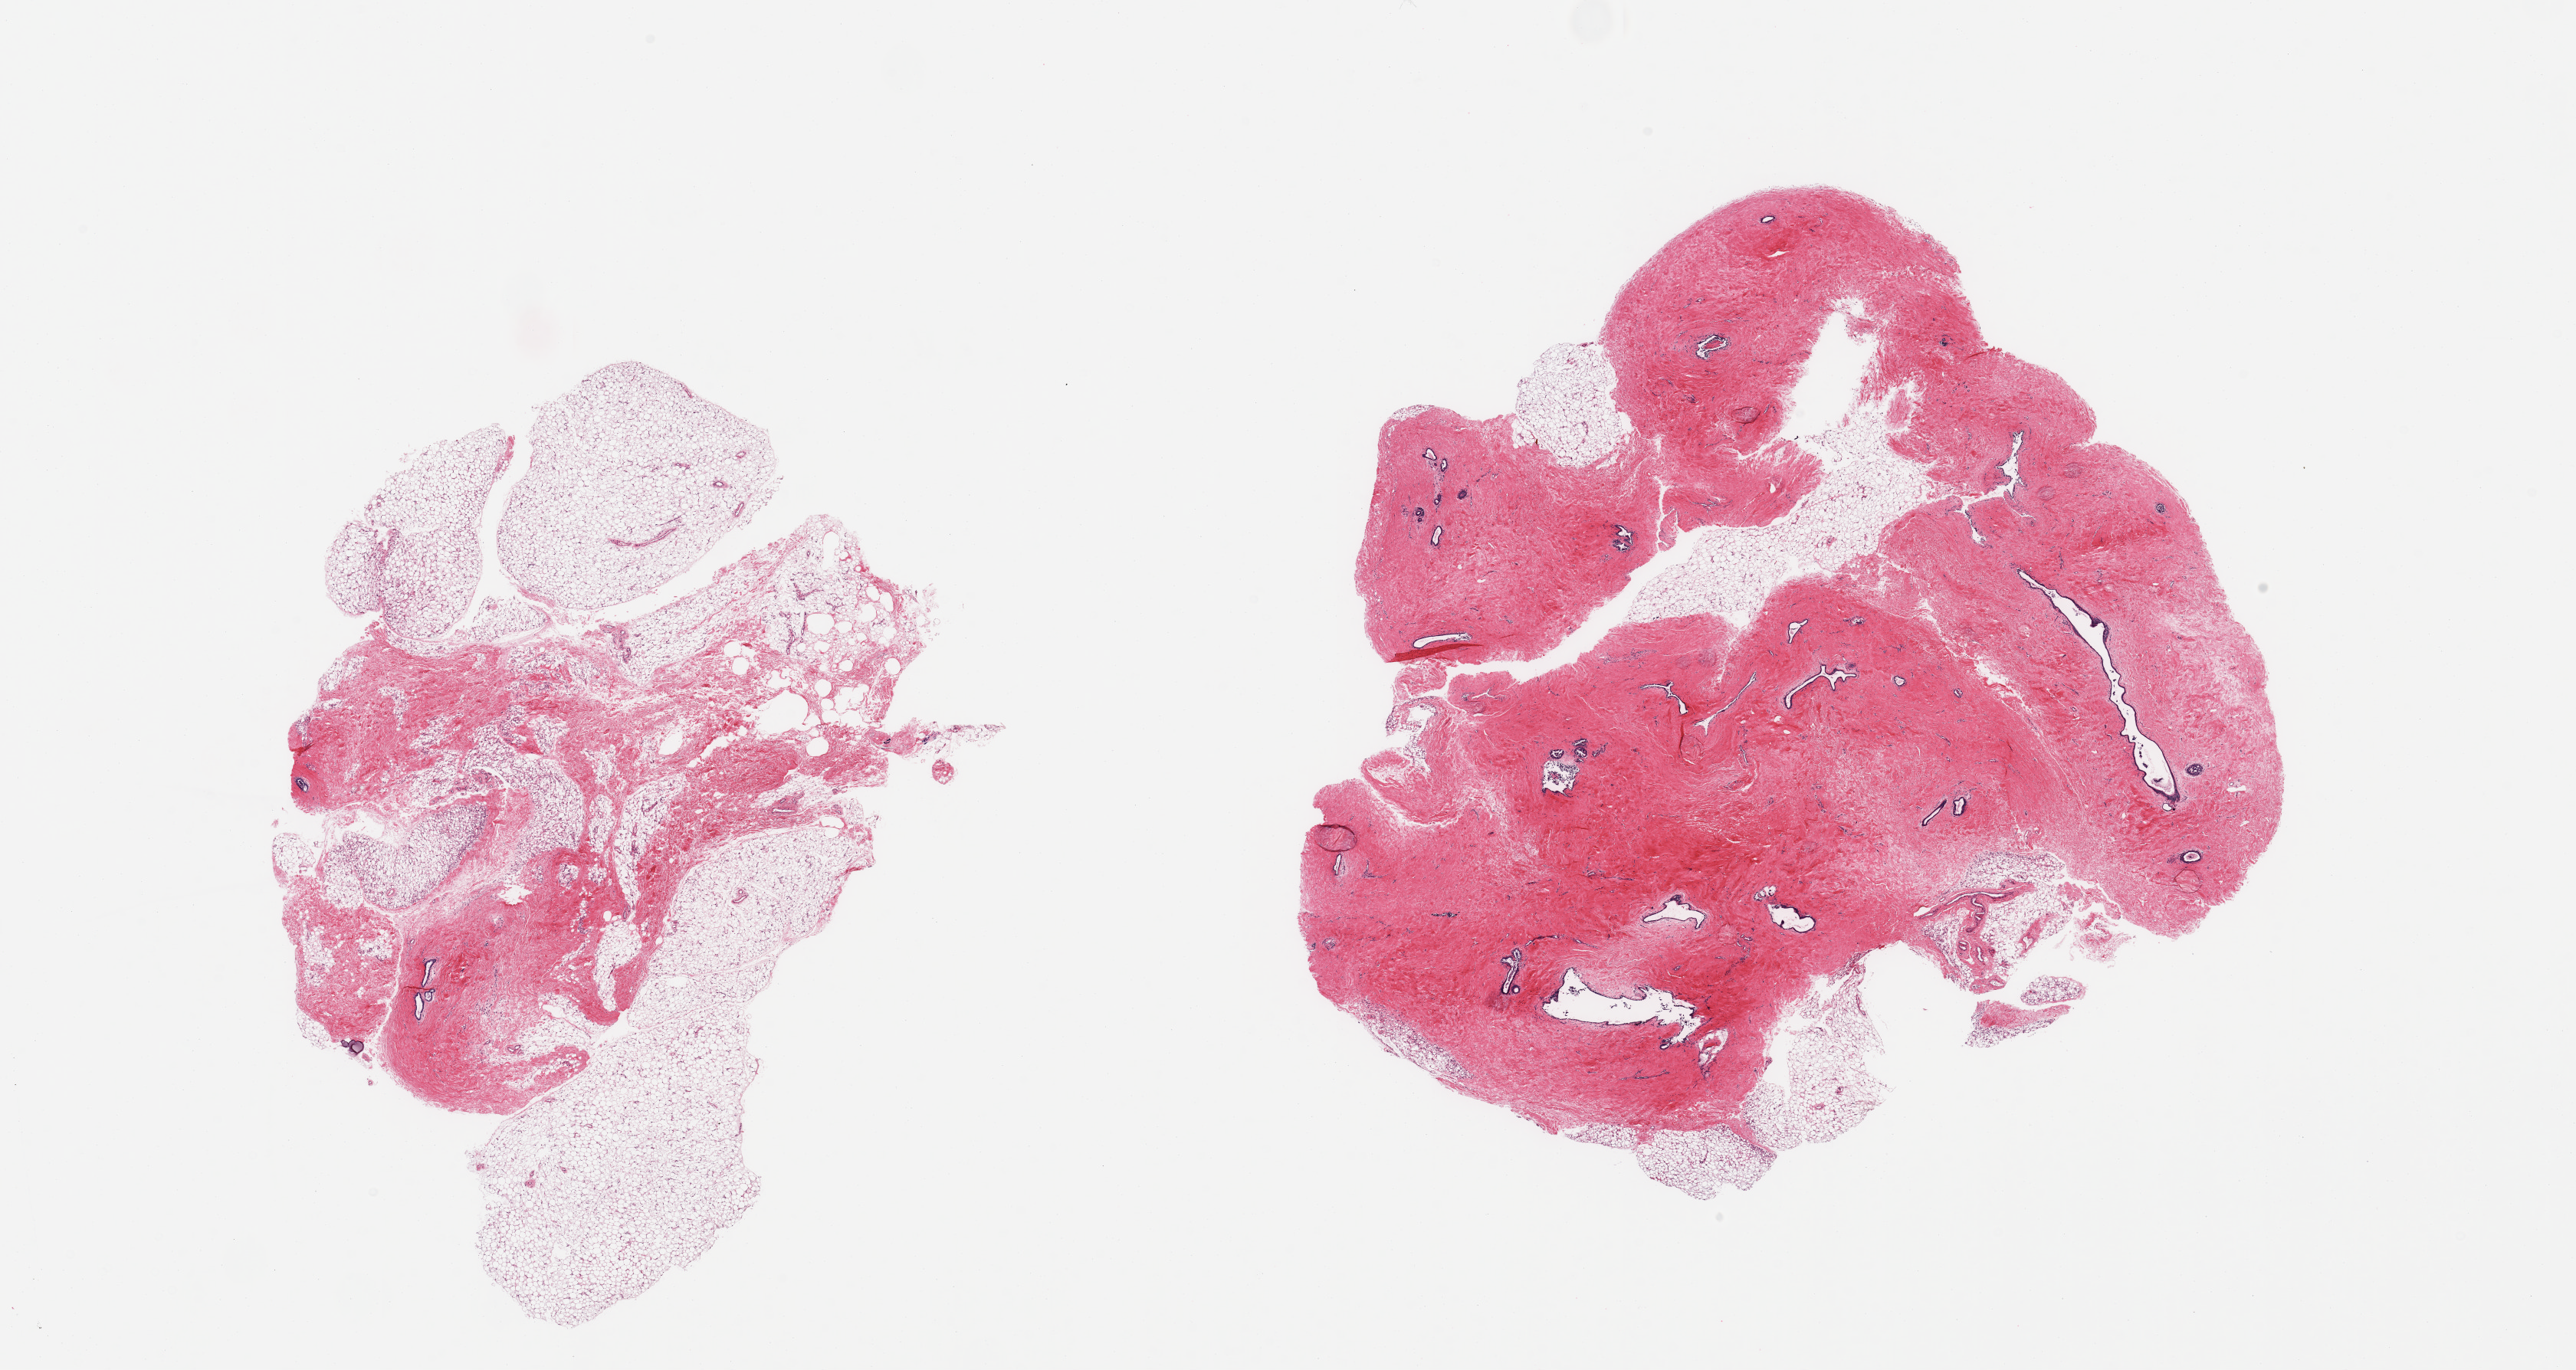
H&E whole-slide image — shown as a low-resolution overview of the whole scanned area (about 26.6 x 14.1 mm, from a 20x scan). PAXgene-fixed, paraffin-embedded tissue. Section of breast (target tissue). Tissue donor sample. Male donor.
Pathologist's review note for this sample: 2 pieces; dense fibrous stroma and ductal proliferation consistent with gynecomastia, especially in 1 piece.